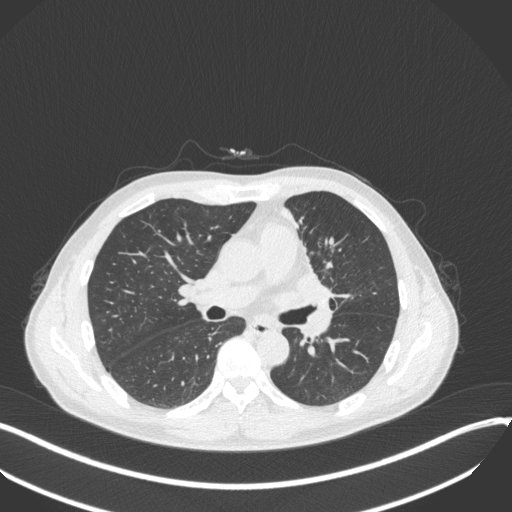
Chest CT, one axial slice; position 187 of 411 along the scan axis; reconstruction kernel B31f; 120 kVp; lung window (W 1500 / L -600 HU); 1 mm slice thickness; 512 × 512 image matrix. Patient: male, 56 years. Case-level facts recorded for this patient, not image findings: clinical TNM (as recorded): T2a N0 M0.
Structures marked on this image (rectangle marked by the reading radiologist):
- lung tumour (recorded histology: squamous cell carcinoma): bounding box (x1, y1, x2, y2) in pixels: (273, 268, 338, 304)